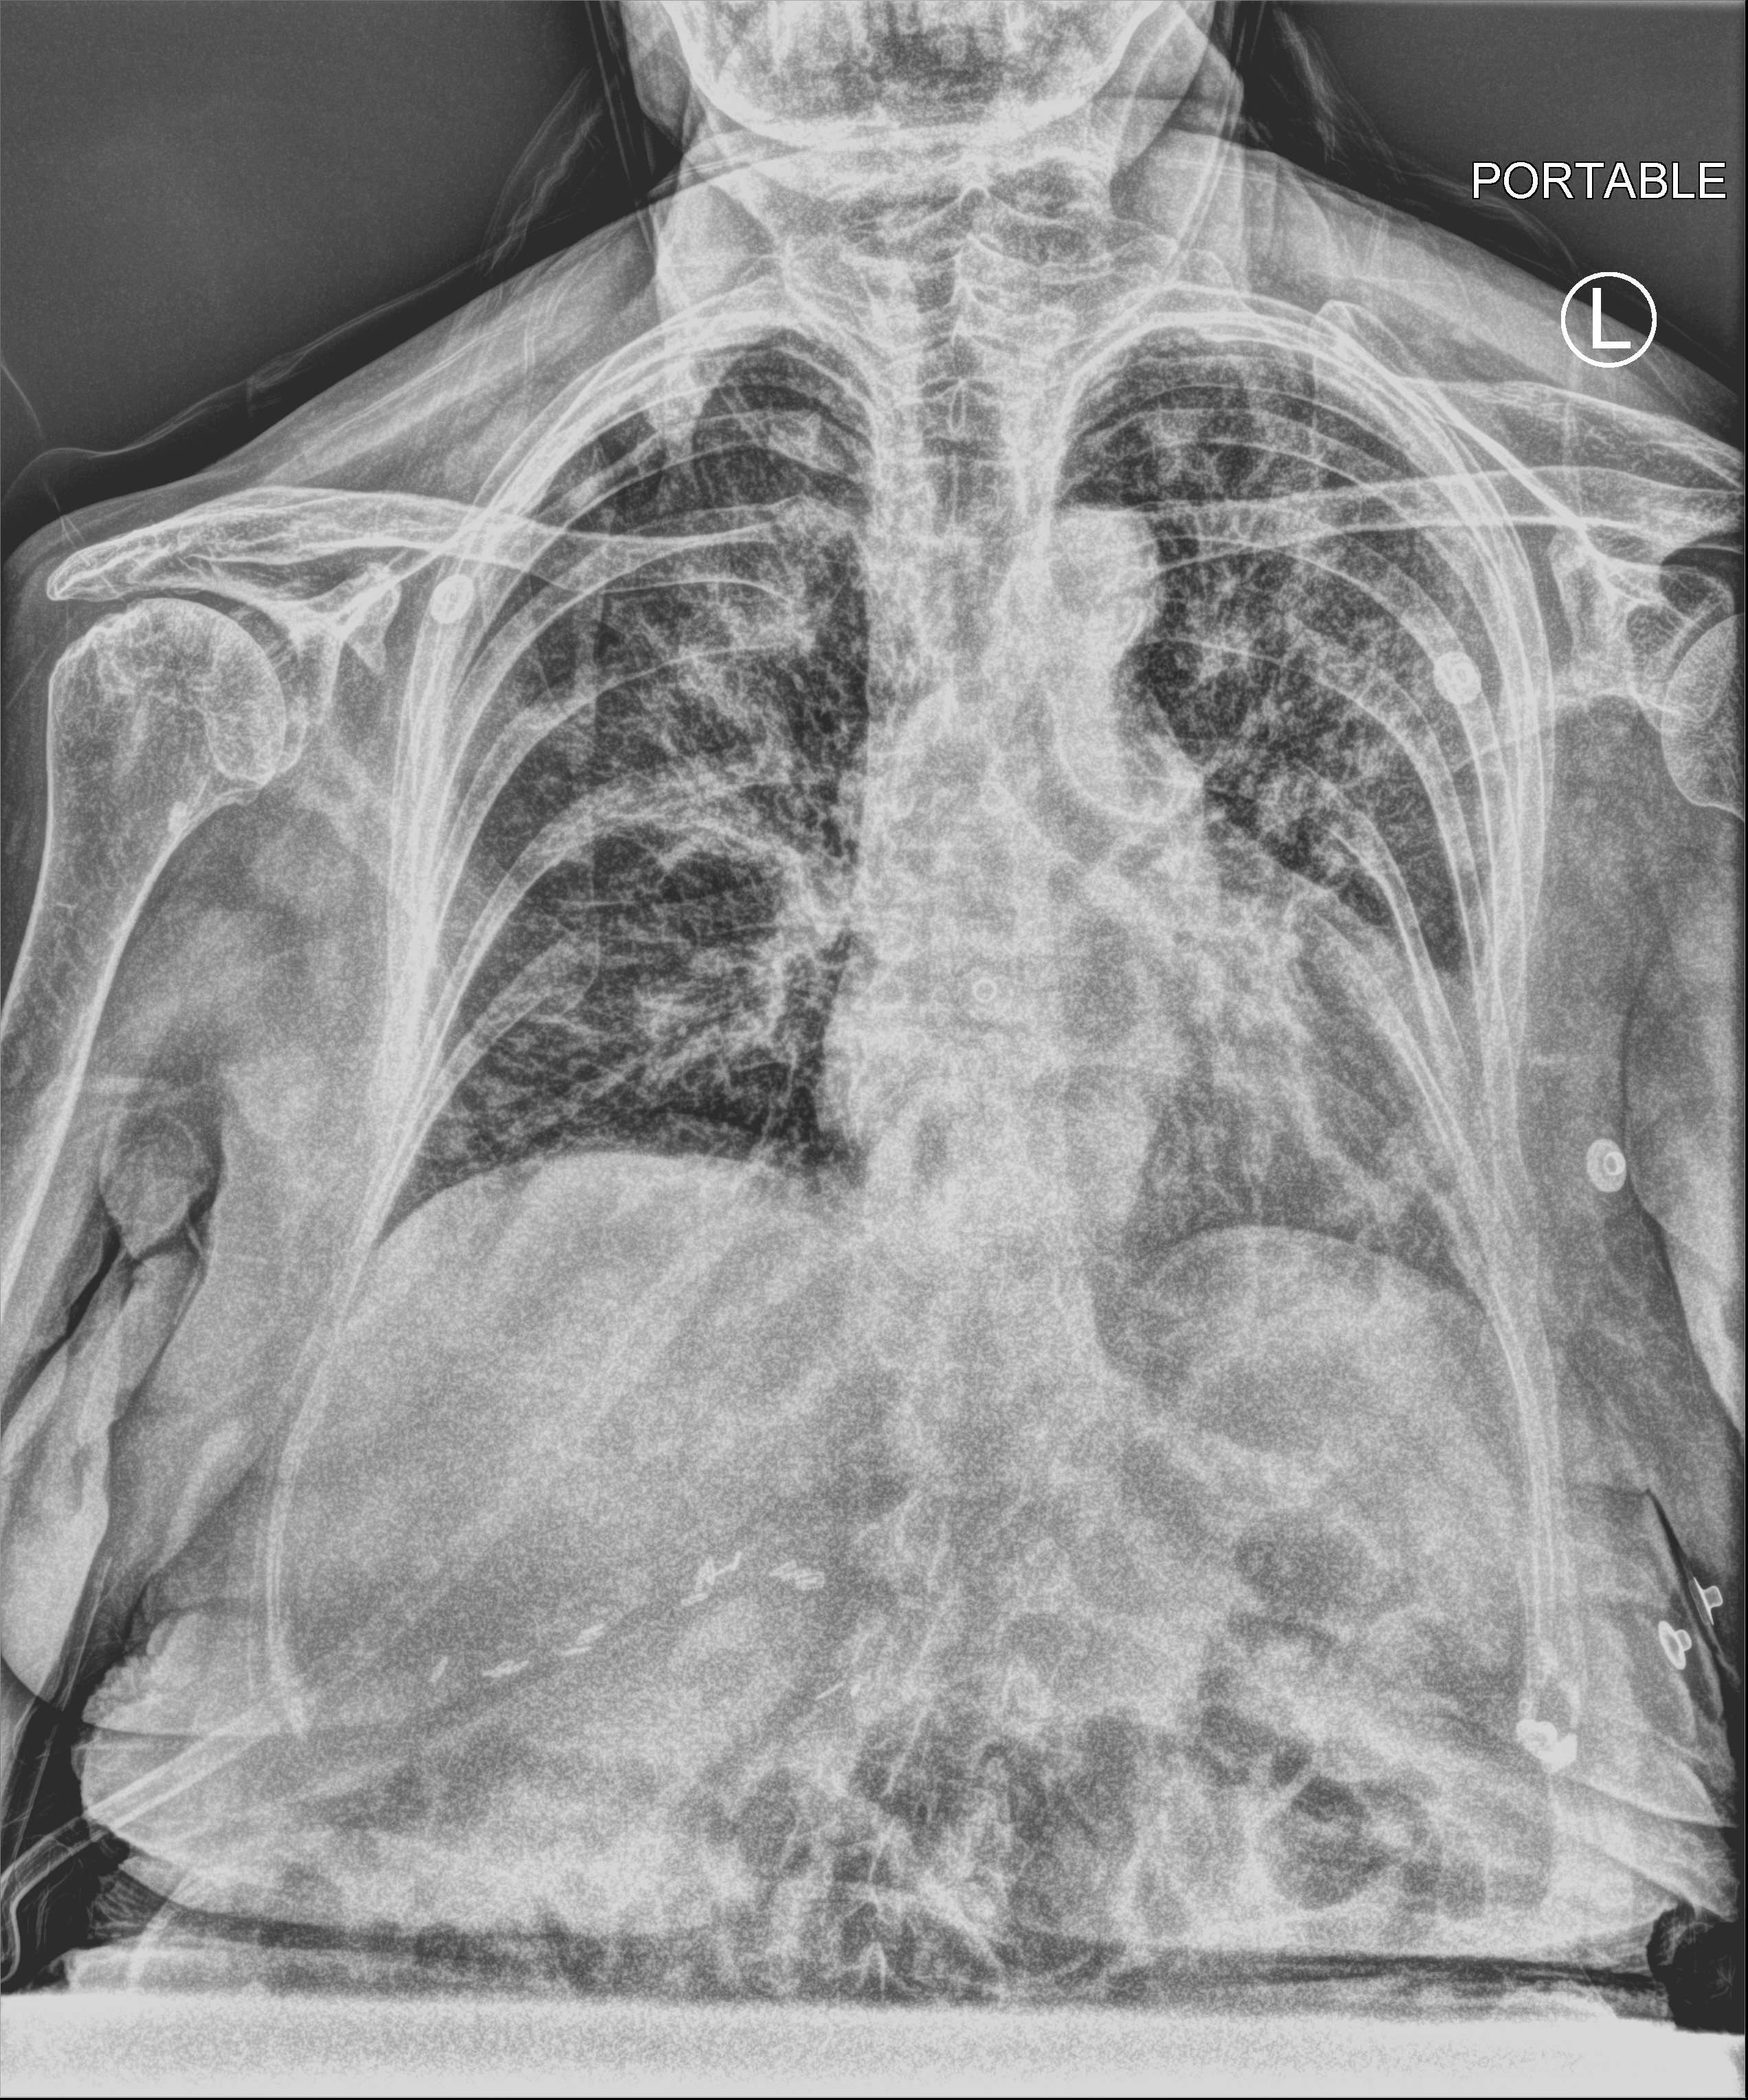
Chest X-ray (portable); anteroposterior (AP) projection. Patient hospitalised with COVID-19; female, aged 75–90 years.
Hospital-stay facts (about this admission, not read from this image; timing relative to this image not recorded):
- diabetes (admission record): no
- hypertension (admission record): yes